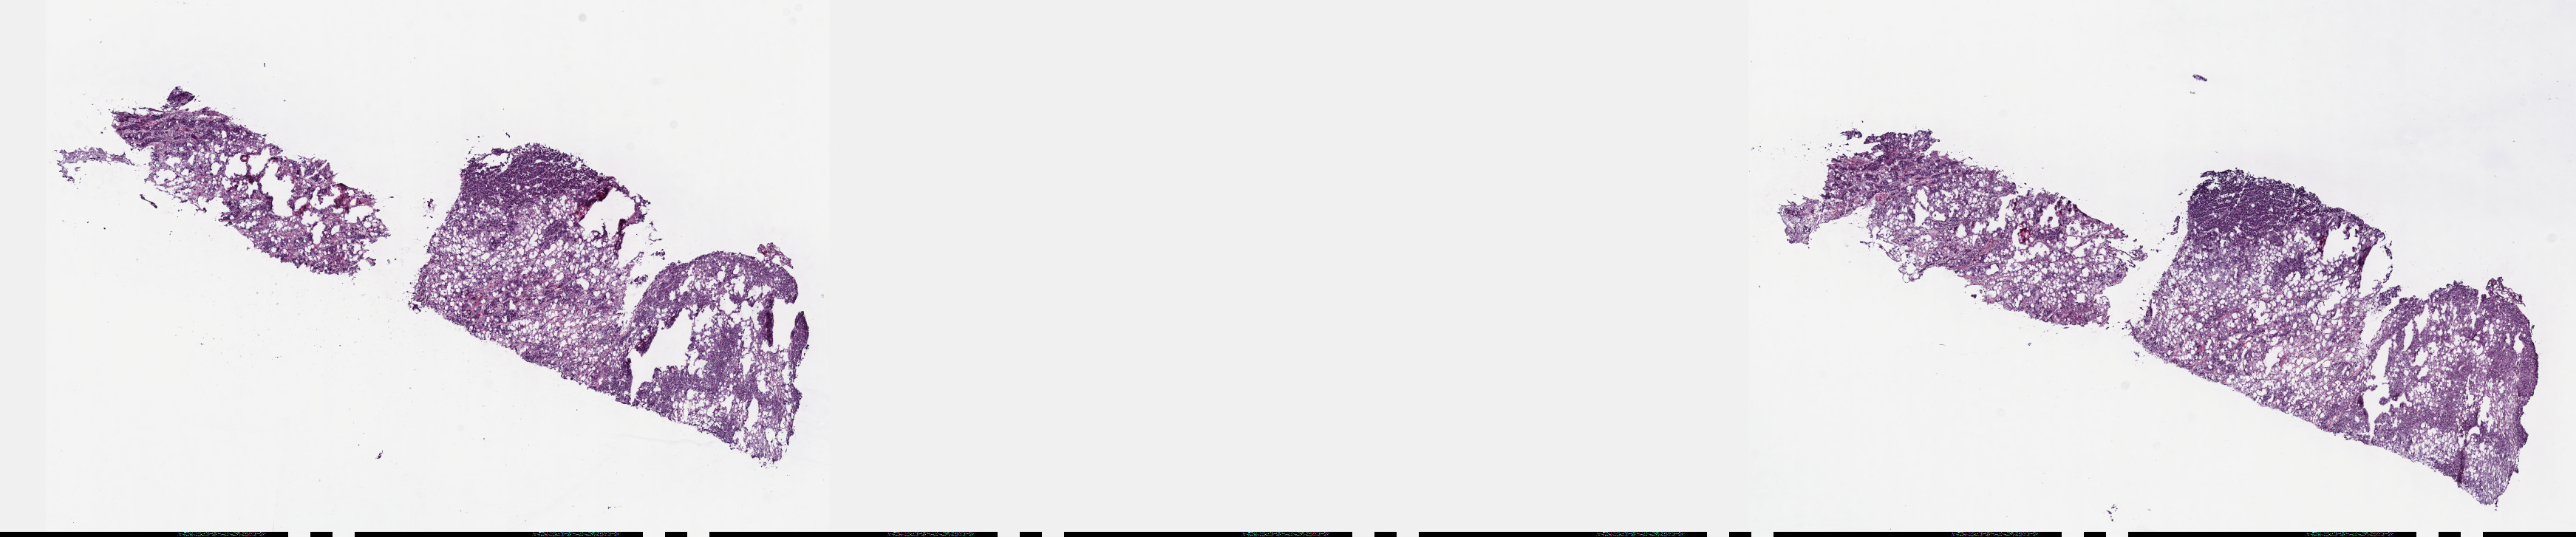
Hematoxylin and eosin (H&E) stained whole-slide image, low-resolution overview of the scanned area, about 28.2 x 5.9 mm (slide scanned at 40x); frozen section; primary tumour sample from the liver. Male, age 54 years at initial diagnosis. Histologic grade: G2 (moderately differentiated). Composition of this section per pathologist review: tumour cells 85%, tumour nuclei 85%, normal cells 0%, stromal cells 15%, necrosis 0%. Infiltration values recorded for this section: lymphocyte infiltration 2%, monocyte infiltration 1%, neutrophil infiltration 3%.
TNM: T1 N0 M0. Histologic diagnosis: Hepatocellular carcinoma, NOS. AJCC pathologic stage: I (6th edition).